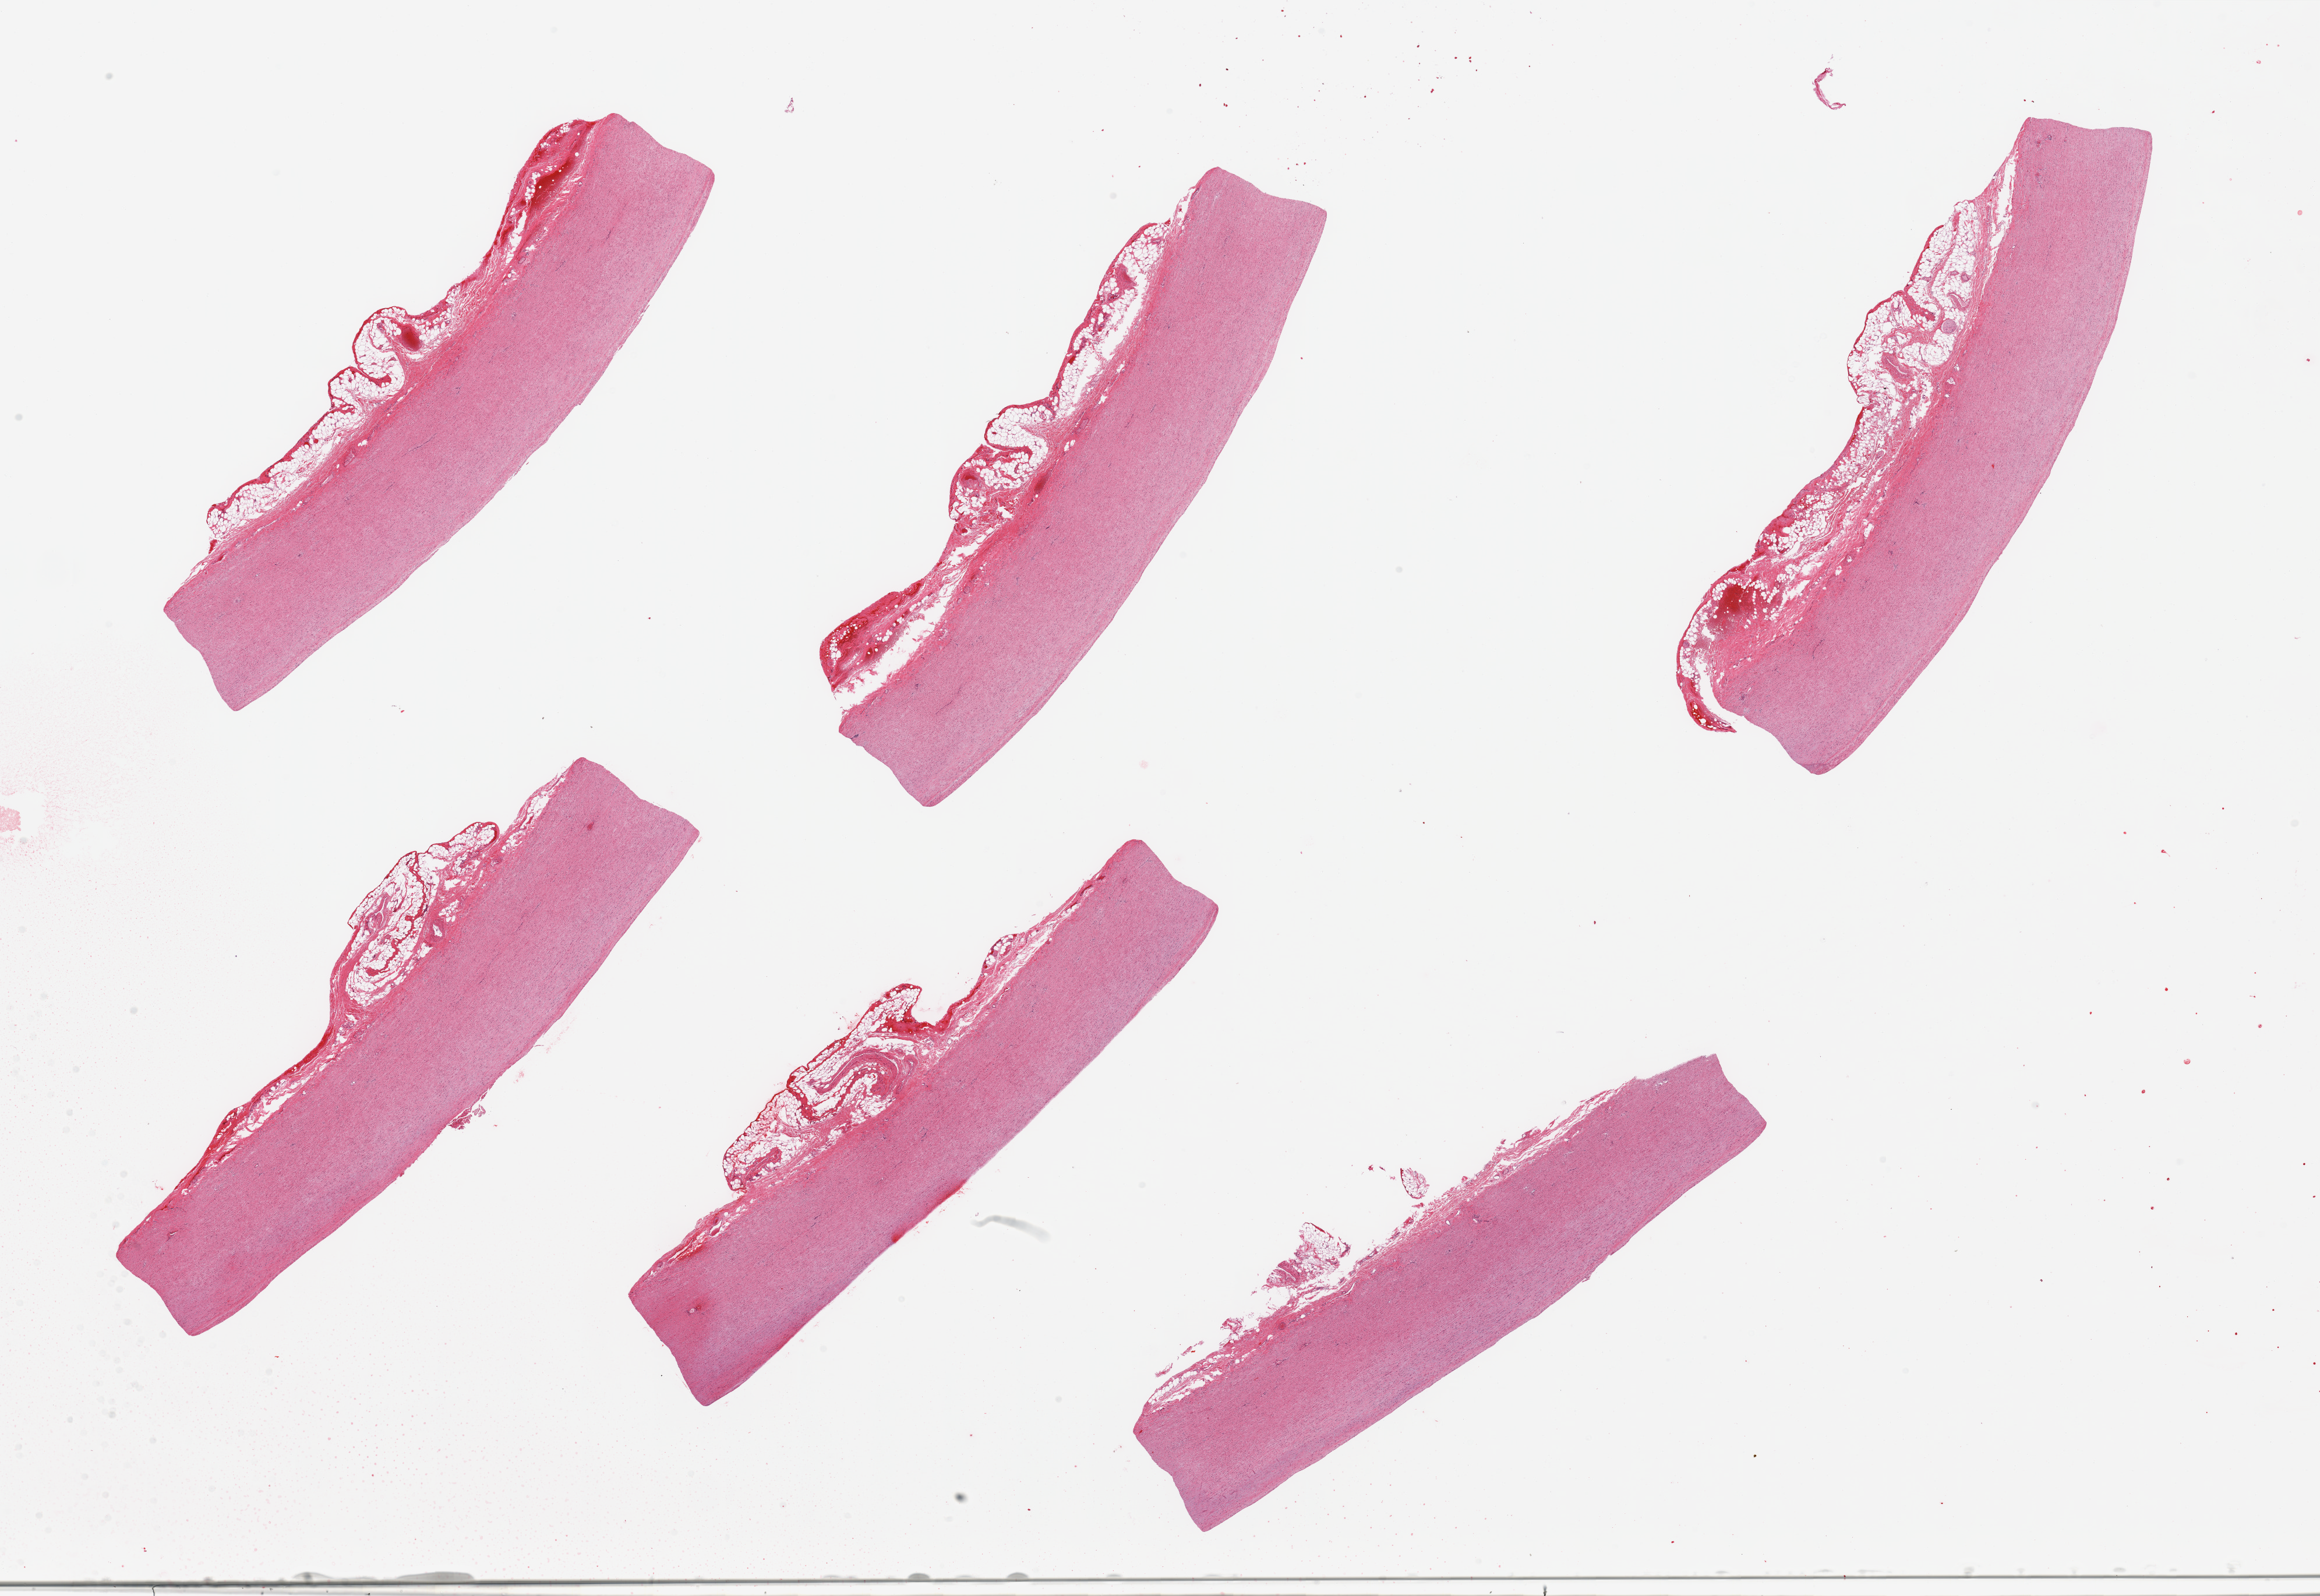
H&E whole-slide image — low-resolution overview of the scanned area, about 31.5 x 21.7 mm; PAXgene-fixed paraffin-embedded (PFPE) section; sampled site (target tissue): aorta; tissue donor sample. Male donor.
Reviewer comment on this tissue sample: 6 pieces; mild plaque, some residual attached fat/adventitia.